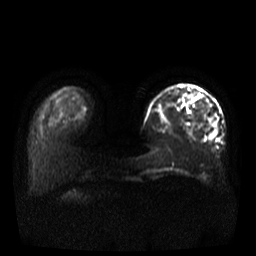
Breast MRI, one axial slice; position 8 of 37 along the scan axis; diffusion-weighted series; image 2 of 4 stored at this slice position (different b-values; order by instance number); 3 T; 5 mm slice thickness; 256 × 256 image matrix, field of view 380 × 380 mm. Female patient.
Annotated regions visible in this slice (manually delineated by an expert):
- tumour on diffusion-weighted imaging: bounding box <209,123,217,140> (left, top, right, bottom; pixels)